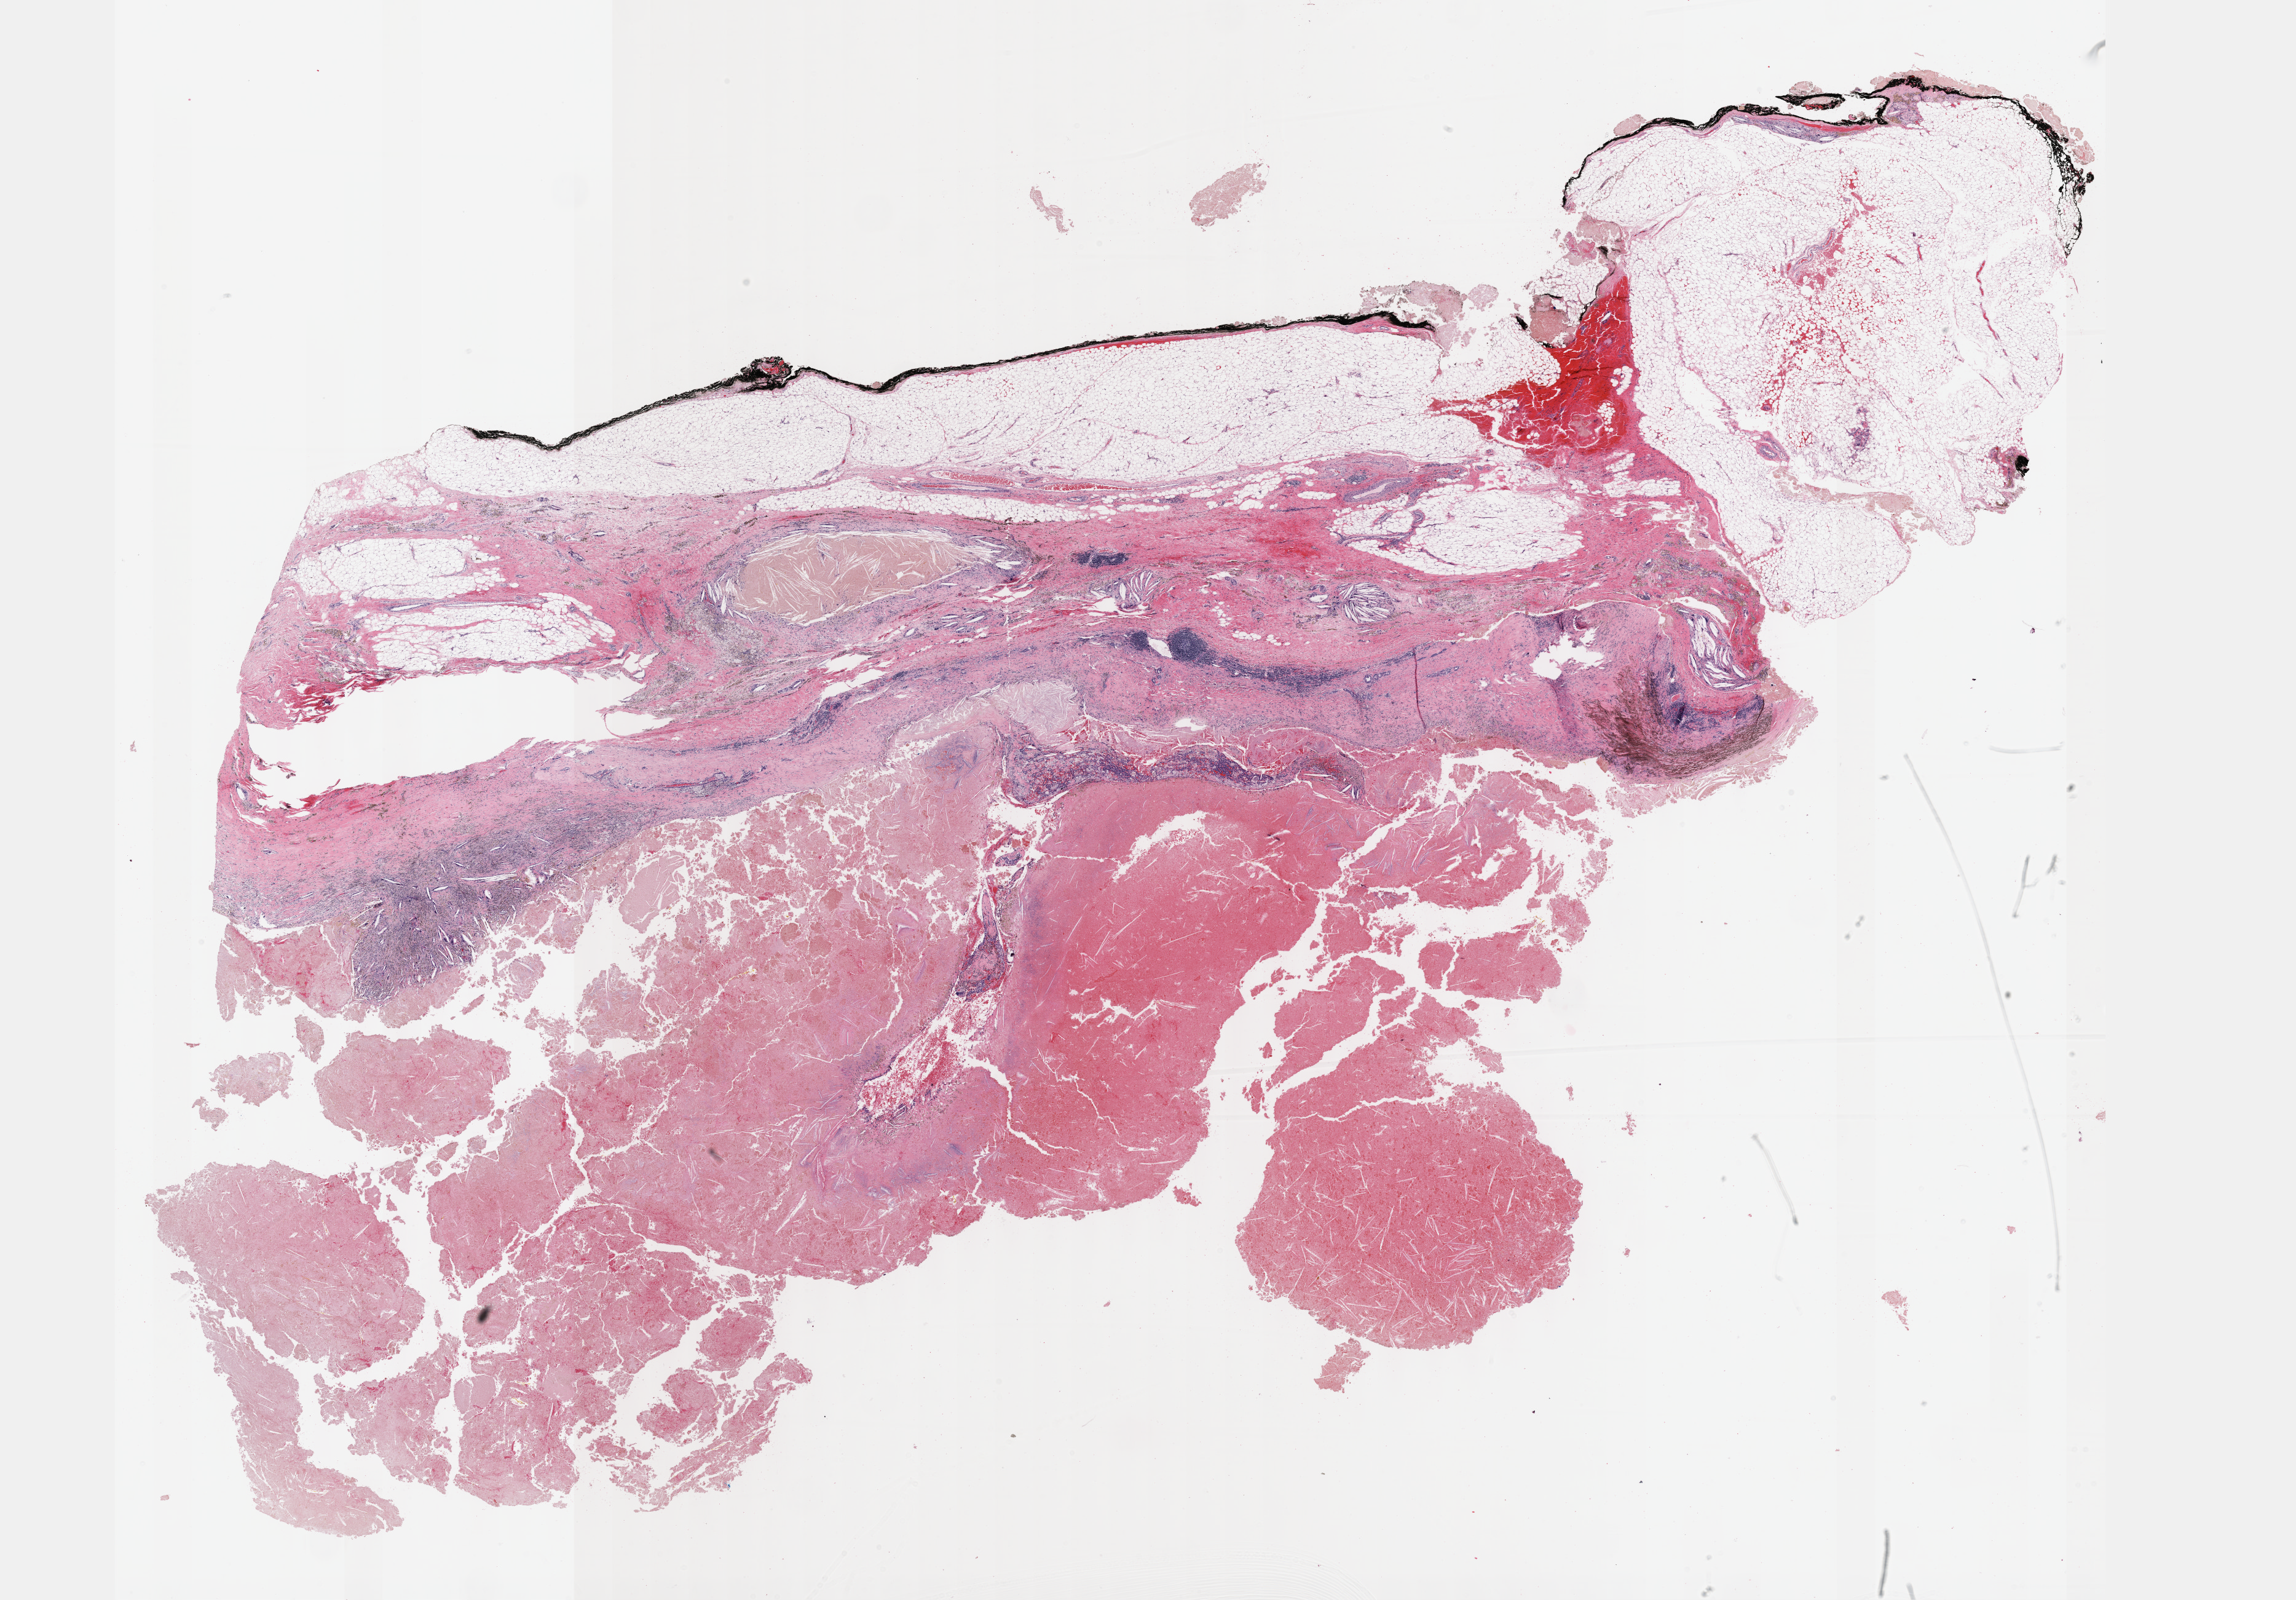
Whole-slide histology image, H&E-stained, whole scanned area (about 30.2 x 21.0 mm, from a 40x scan) shown as a low-resolution overview; formalin-fixed paraffin-embedded (FFPE) diagnostic section; primary tumour sample from the kidney. Male patient; age at initial diagnosis 85 years.
Laterality: right. Pathologic diagnosis: Papillary adenocarcinoma, NOS. AJCC pathologic stage: I (7th edition).